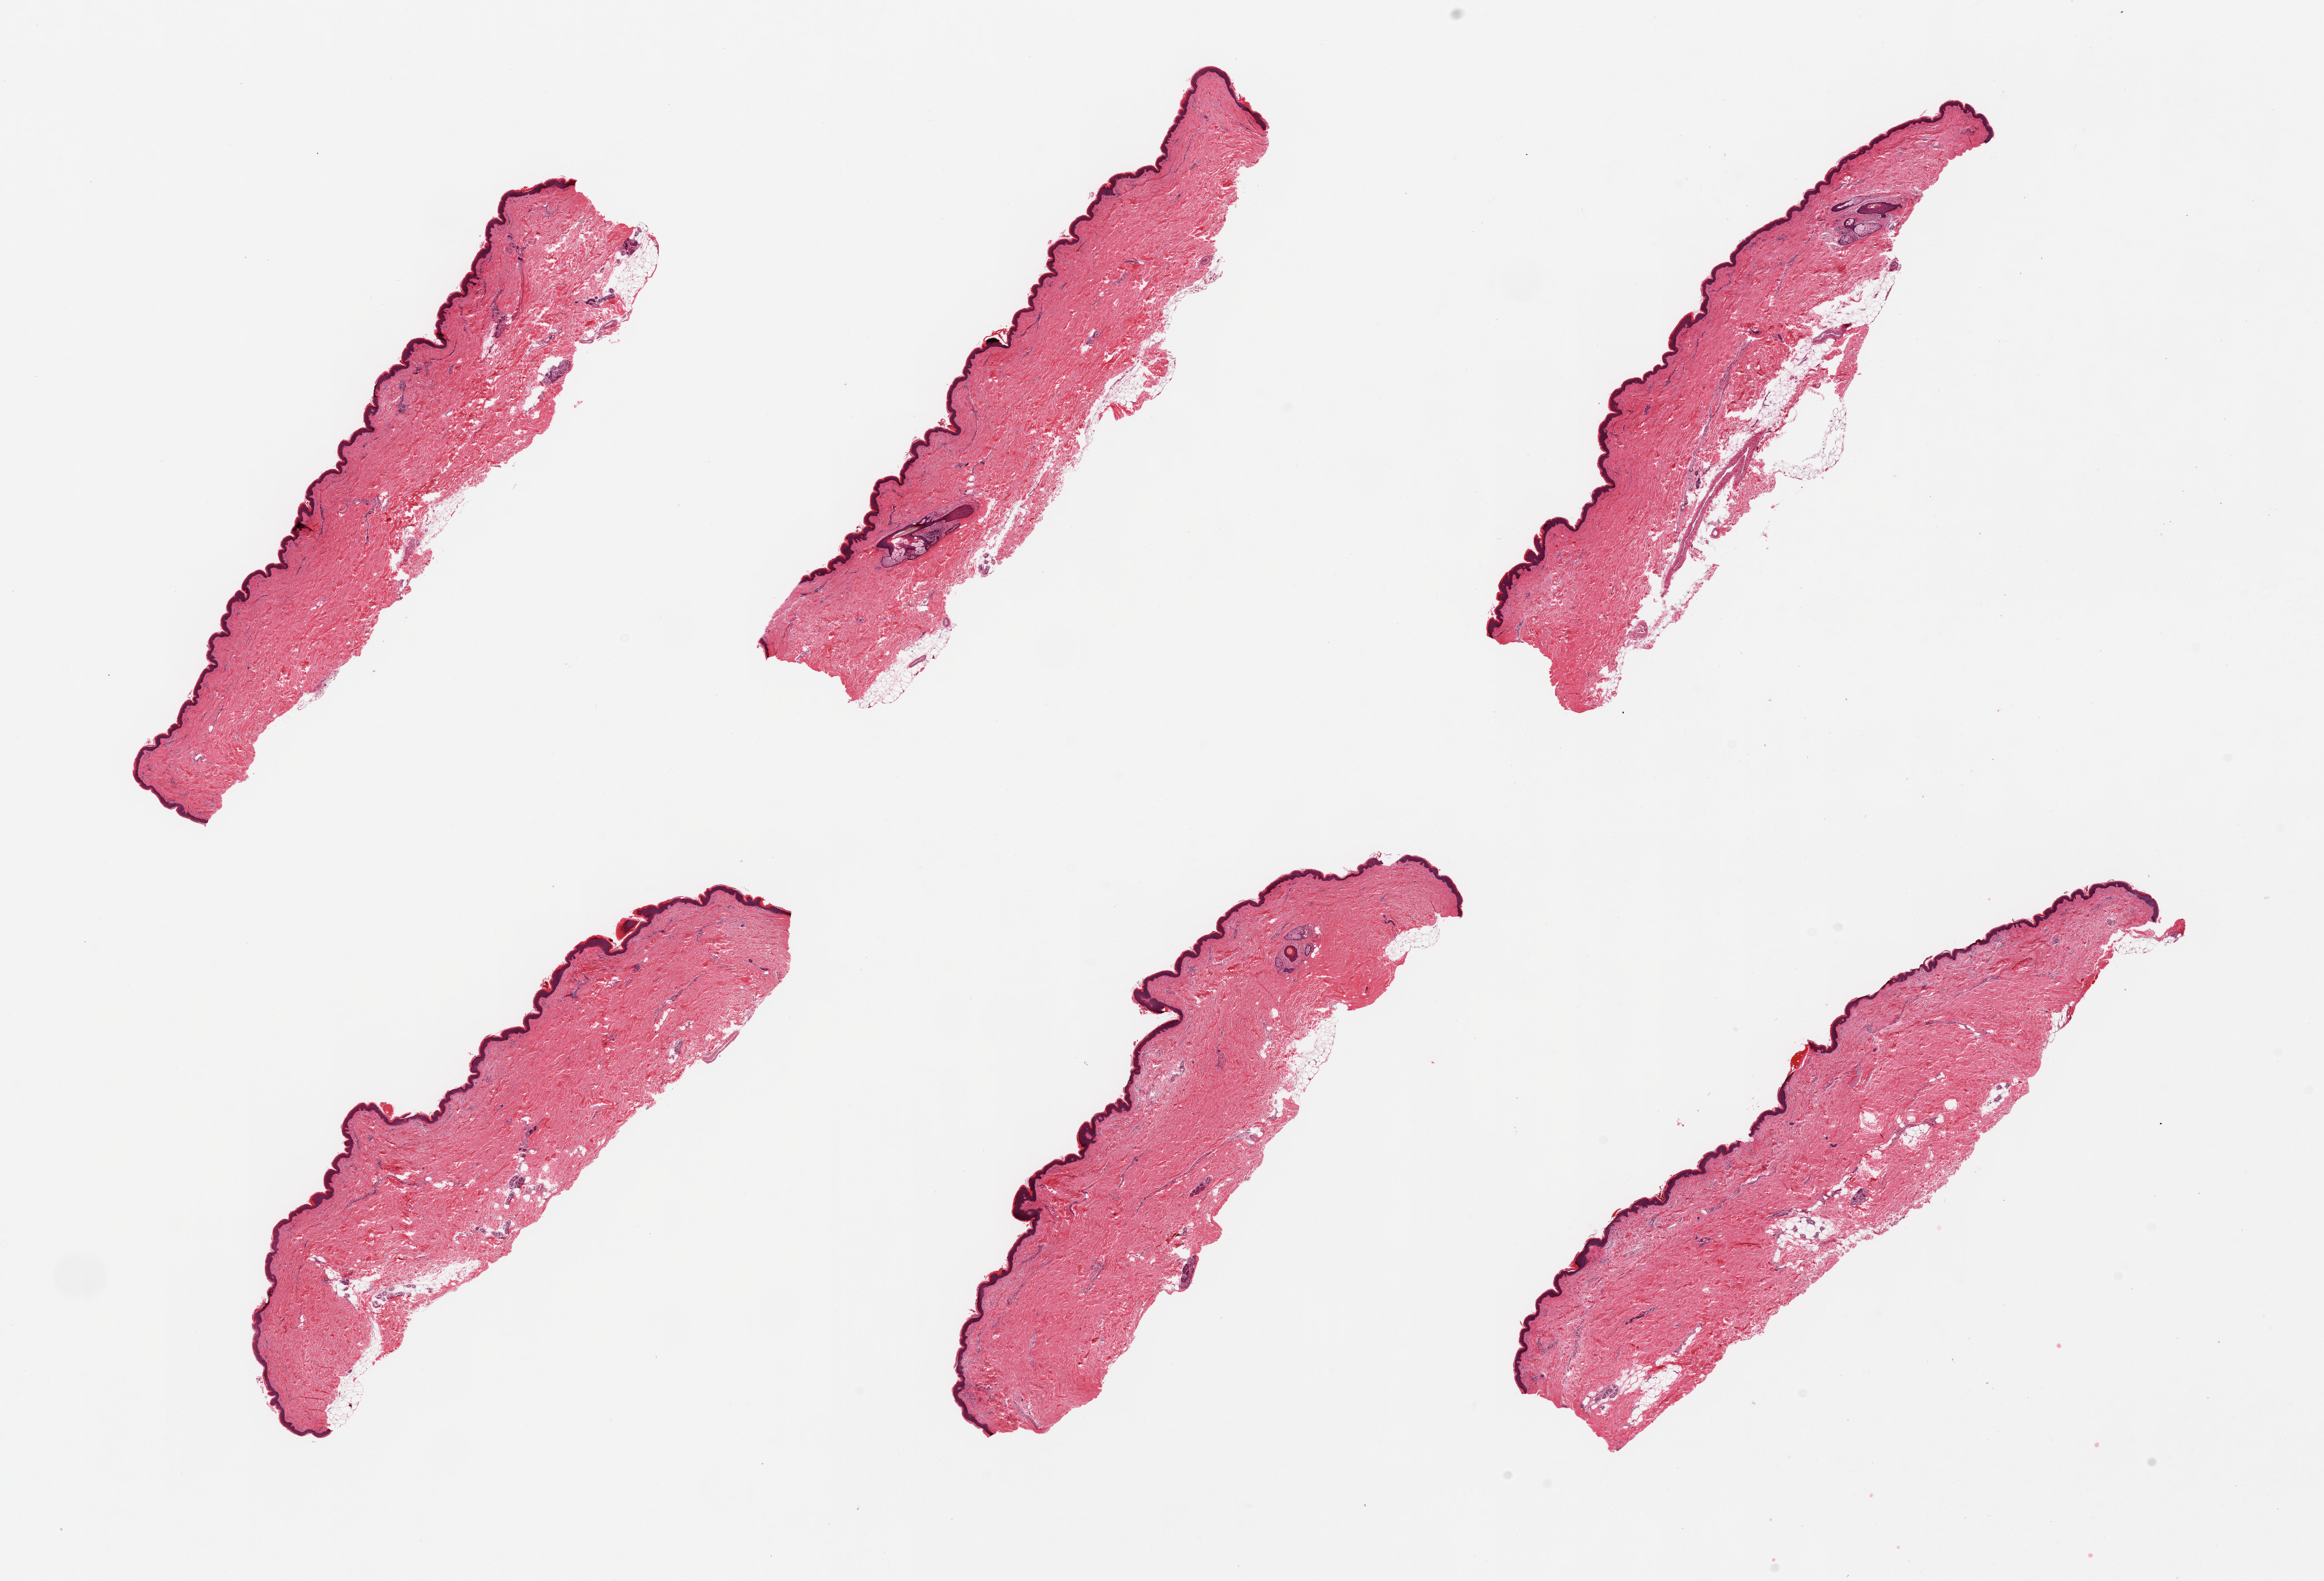
Whole-slide image, haematoxylin and eosin stain, low-resolution overview of the scanned area, about 27.6 x 18.8 mm. PAXgene-fixed paraffin-embedded (PFPE) section. Section of skin of suprapubic region (target tissue). Tissue donor sample. Male donor.
• pathologist's review note for this sample: 6 pieces, minimal dermal fat, squamous epithelium is ~50-60 microns